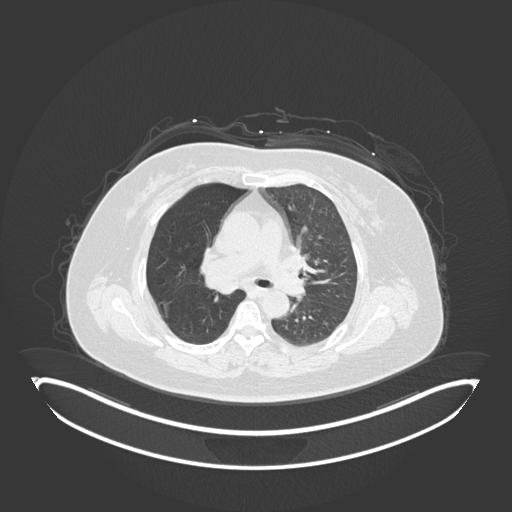
Chest CT, one axial slice; position 102 of 245 along the scan axis; reconstruction kernel B30f; 120 kVp; lung window (W 1500 / L -600 HU); 512 × 512 image matrix, field of view 500 × 500 mm. Female patient, age 60 years. From the clinical record (not read from this slice): clinical TNM (as recorded): T1c N0 M0; histopathological grade: G1-G2.
Structures marked on this image (rectangle marked by the reading radiologist):
- lung tumour (recorded histology: squamous cell carcinoma): box from (x=204, y=268) to (x=244, y=296) px